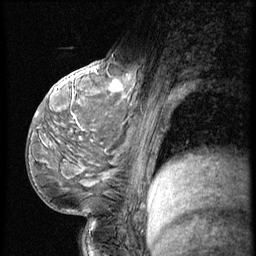
Breast MRI (dynamic contrast-enhanced), one sagittal slice. 3 images stored at this slice position (order not interpretable as contrast timing). 1.5 T. TE 4.2 ms, TR 9 ms. 256 × 256 image matrix, field of view 180 × 180 mm. Female patient, age 54 years. Case-level facts recorded for this patient, not image findings: setting: breast cancer imaged before/during neoadjuvant chemotherapy; receptor status: triple-negative.
Structures marked on this image (semi-automatic segmentation, software-assisted and operator-edited):
- analysis volume of interest (the breast-tissue region the enhancement analysis was run in; not a lesion): bounding box [x1, y1, x2, y2] px = [99, 53, 149, 102]
- tumour enhancement mask (voxels above the 140 % enhancement threshold inside the analysis volume of interest): [111, 68, 138, 95]